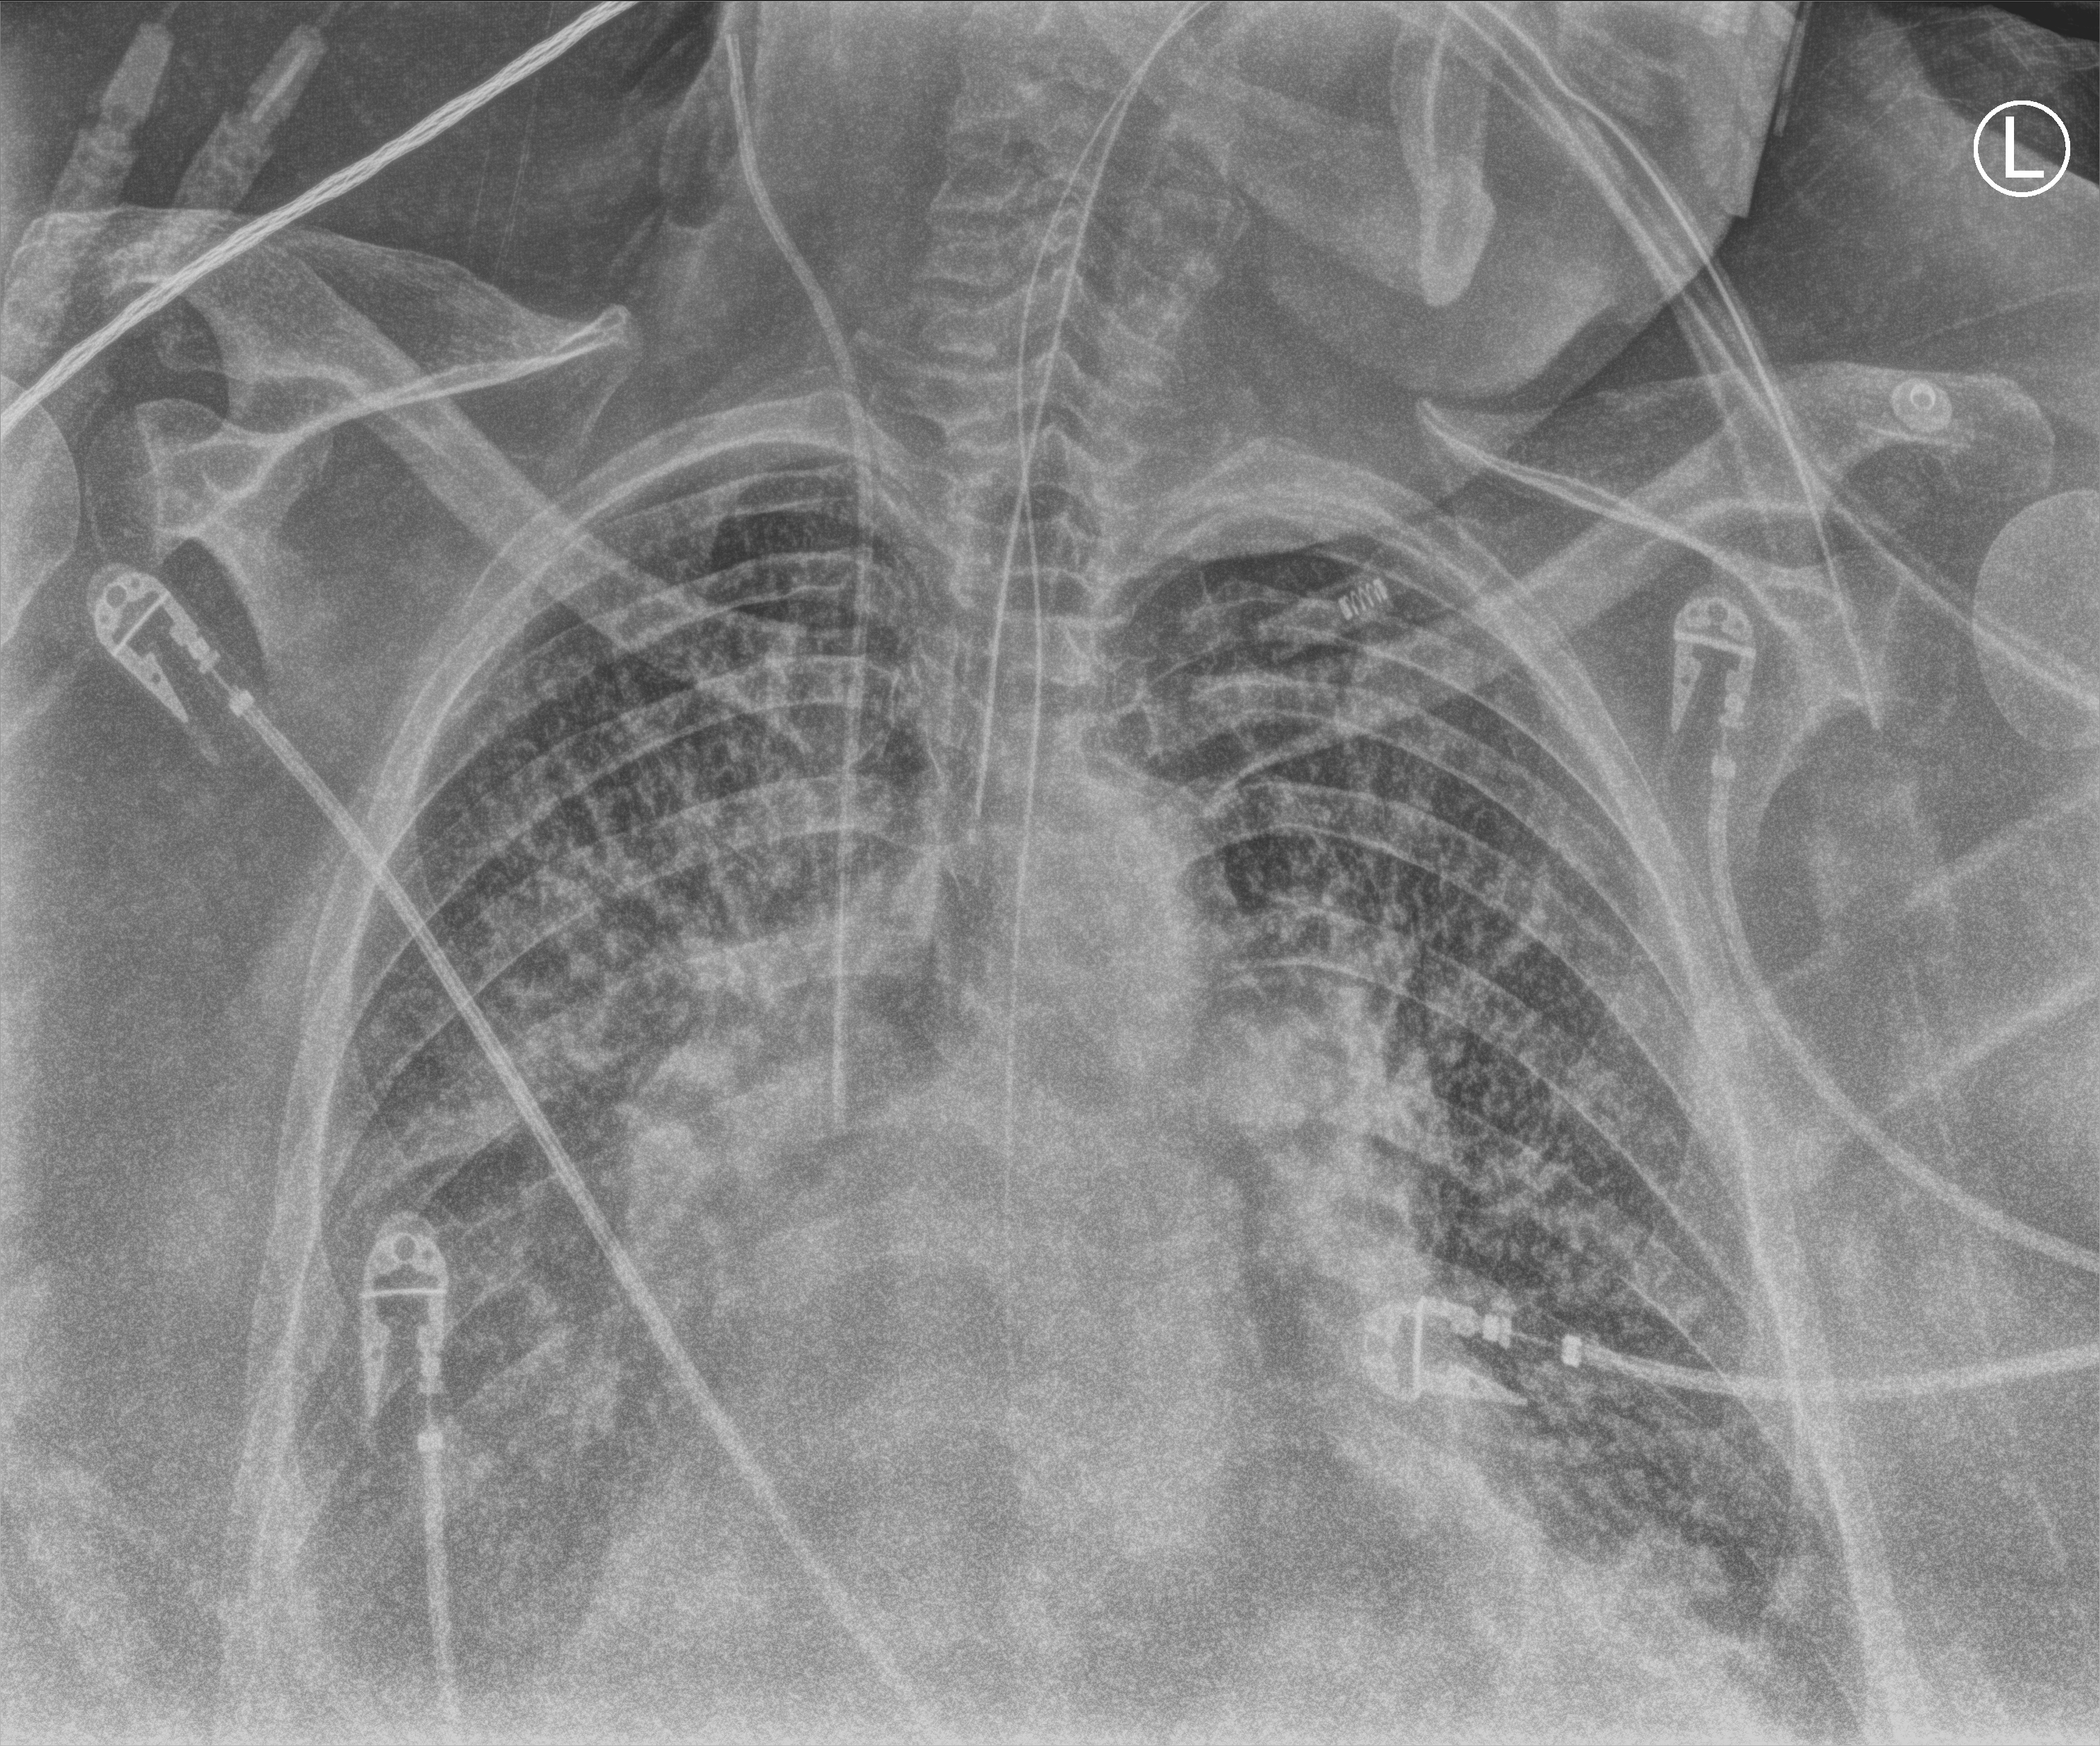
Bedside chest radiograph (computed radiography), anteroposterior (AP) projection. Patient hospitalised with COVID-19; female, aged 60–74 years.
From the hospital-stay record, not from the radiograph (when in the stay this image was taken is not recorded): admitted to intensive care during this hospital stay: yes.